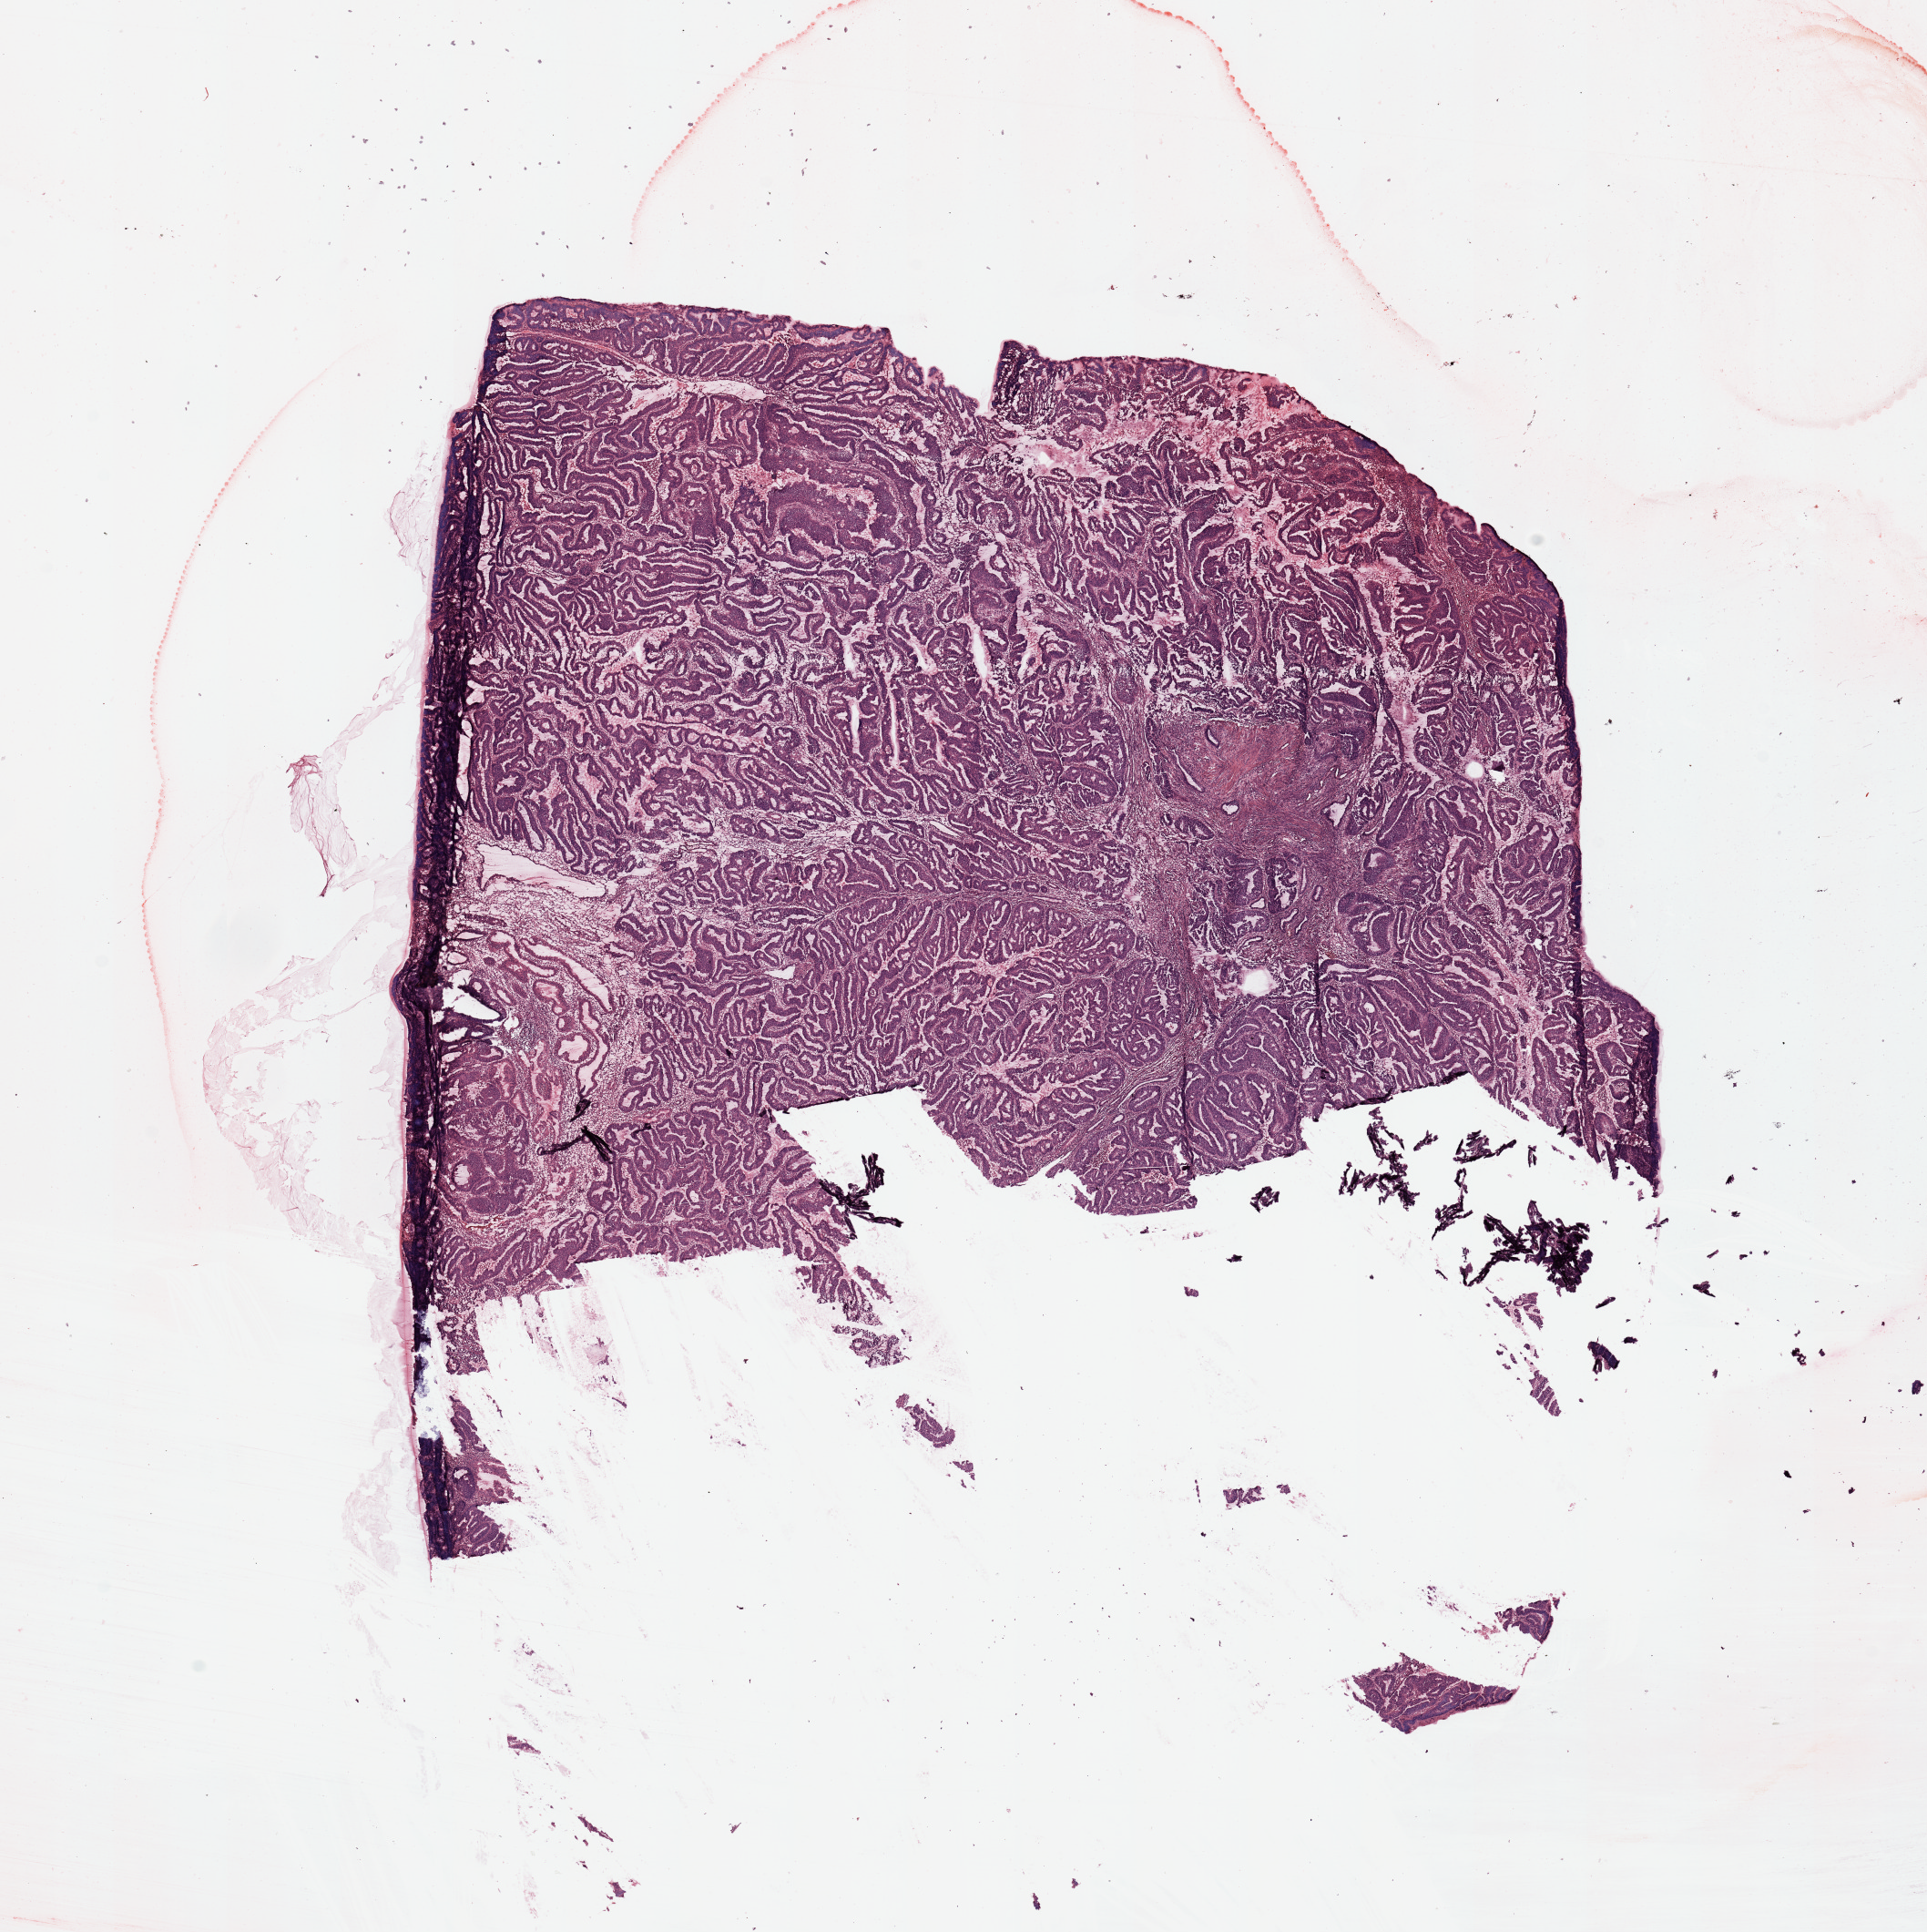
Whole-slide histology image, H&E-stained — low-resolution overview of the scanned area, about 16.7 x 16.8 mm (from a 20x scan). Tumour tissue sample, uterus. 45-year-old female patient. Histologic grade: G1 (well differentiated).
* diagnosis: Endometrioid adenocarcinoma, NOS
* AJCC pathologic stage: I